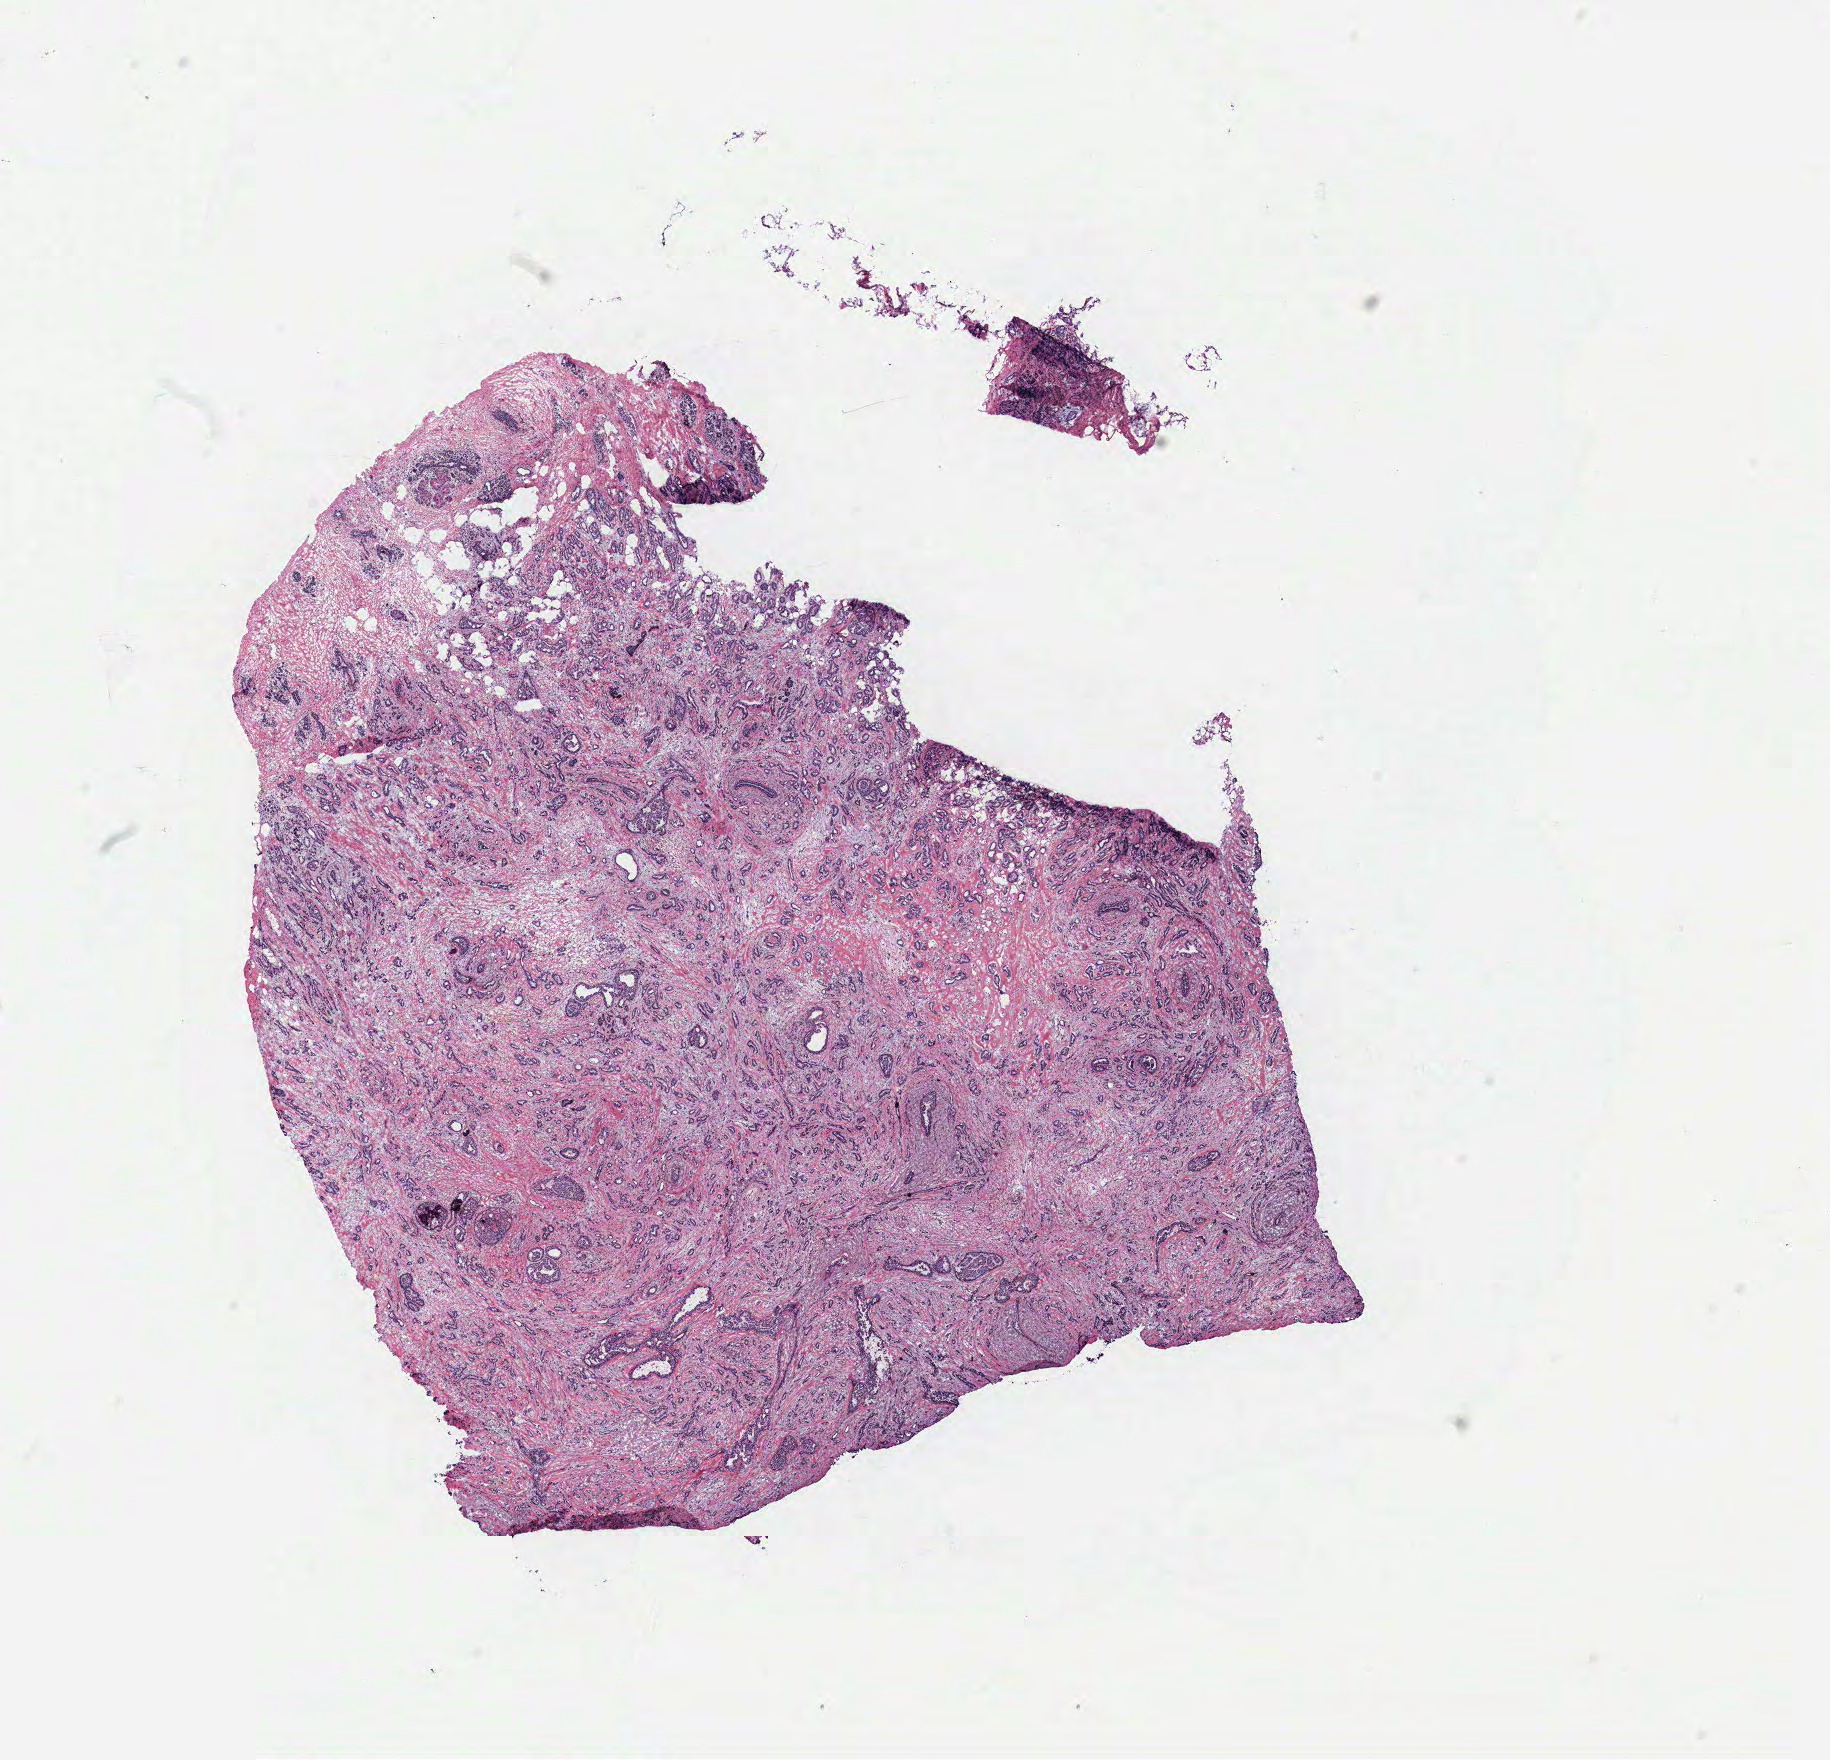
H&E-stained whole-slide image, a low-resolution overview of the entire scanned area, about 14.6 x 14.1 mm (acquisition: 40x scan); breast, tissue type not recorded.
Patient diagnosis (cohort enrolment): breast cancer (breast).